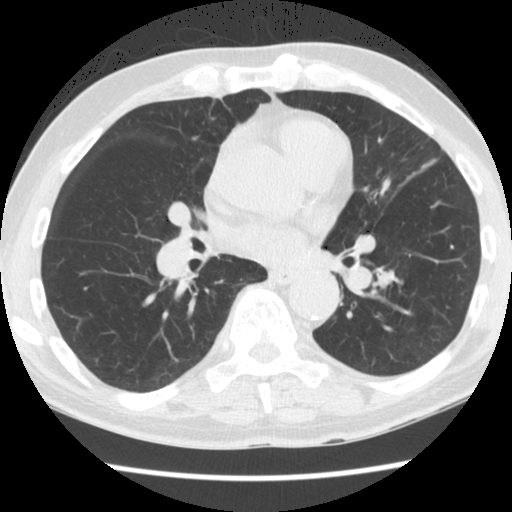
Low-dose screening chest CT, one axial slice. Slice 80 of 174 in the series (ordered by position). Reconstruction kernel STANDARD. 120 kVp. Lung window (W 1500 / L -600 HU). 2.5 mm slice thickness. 512 × 512 image matrix, field of view 320 × 320 mm.
Structures marked on this image (expert manual segmentation):
- lesion 1 (tumor, lower lobe of left lung): box from (x=378, y=269) to (x=395, y=286) px